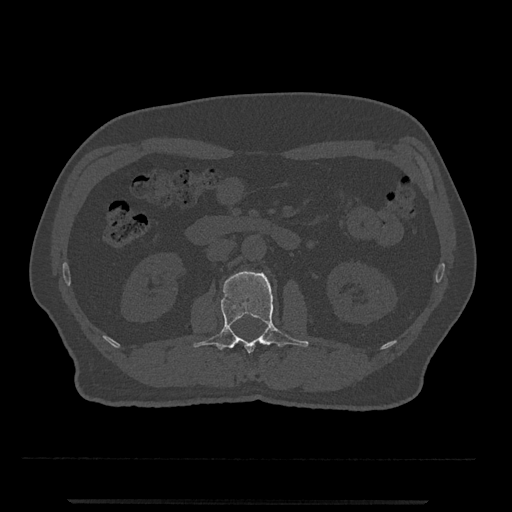
CT including the spine, one axial slice. Position 271 of 797 along the scan axis. 120 kVp. Bone window (W 1800 / L 400 HU). 0.5 mm slice thickness. 512 × 512 image matrix, field of view 419 × 419 mm. Male patient, age 63 years. Case-level facts recorded for this patient, not image findings: primary cancer: prostate.
Outlined on this slice (semi-automatically segmented with operator editing):
- L2 vertebra: bounding box (x1, y1, x2, y2) in pixels: (193, 271, 309, 353)